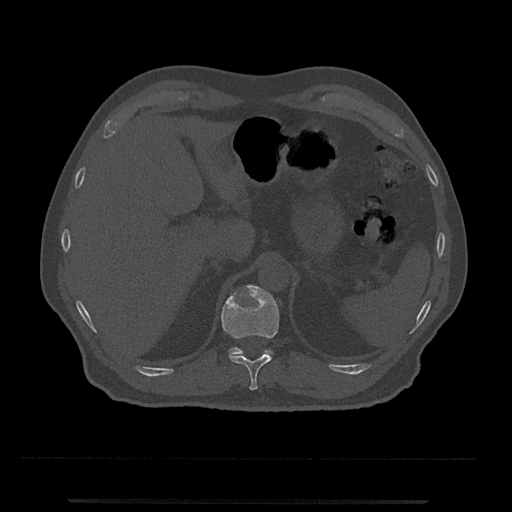
CT including the spine, one axial slice. Position 447 of 797 along the scan axis. Reconstruction kernel Br40s/3. Bone window (W 1800 / L 400 HU). 0.5 mm slice thickness. 512 × 512 image matrix. Male patient, age 63 years. Case-level facts recorded for this patient, not image findings: primary cancer: prostate.
Annotated regions visible in this slice (semi-automatic segmentation, software-assisted and operator-edited):
- T11 vertebra: bounding box <221,285,280,390> (left, top, right, bottom; pixels)
- T12 vertebra: <229,347,273,356>